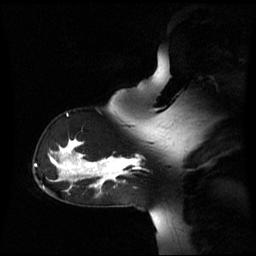
Breast MRI (dynamic contrast-enhanced), one sagittal slice; position 44 of 60 along the scan axis; dynamic contrast-enhanced series, image 2 of 3 at this slice position (ordered by acquisition); 1.5 T; TE 4.2 ms, TR 8.4 ms; 2.6 mm slice thickness; 256 × 256 image matrix, field of view 270 × 270 mm. Female patient, age 39 years. From the clinical record (not read from this slice): setting: breast cancer imaged before/during neoadjuvant chemotherapy; receptor status: triple-negative.
Outlined on this slice (semi-automatic segmentation, software-assisted and operator-edited):
- analysis volume of interest (the breast-tissue region the enhancement analysis was run in; not a lesion): bounding box (x1, y1, x2, y2) in pixels: (105, 157, 139, 179)
- tumour enhancement mask (voxels above the 70 % enhancement threshold inside the analysis volume of interest): (105, 157, 138, 179)